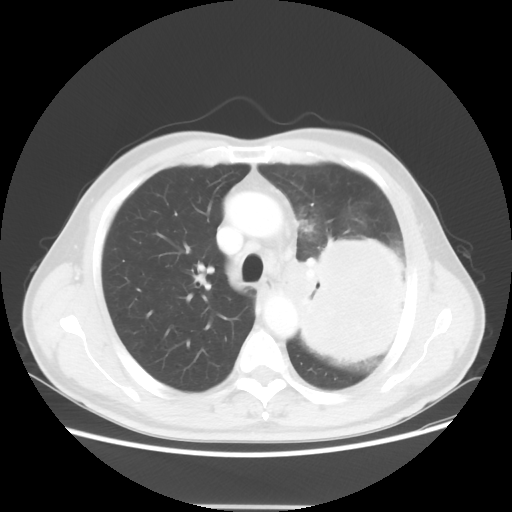
Chest CT, one axial slice; position 37 of 53 along the scan axis; reconstruction kernel STANDARD; 100 kVp; lung window (W 1500 / L -600 HU); 512 × 512 image matrix. Male patient, age 60 years. Case-level facts recorded for this patient, not image findings: clinical TNM (as recorded): T4 N1 M1a; histopathological grade: G3.
Annotated regions visible in this slice (bounding box drawn by a radiologist):
- lung tumour (recorded histology: large cell carcinoma): box from (x=287, y=232) to (x=415, y=373) px